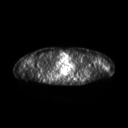
FDG PET of an extremity soft-tissue mass (from a PET/CT study), one axial slice. Position 199 of 267 along the scan axis. 128 × 128 image matrix, field of view 600 × 600 mm. Female patient, age 28 years. Case-level facts recorded for this patient, not image findings: histological type: malignant fibrous histiocytoma; grade: low; site of the primary tumour: left arm.
Outlined on this slice (expert contour drawn on MRI and transferred to this co-registered scan by the dataset authors):
- gross tumour volume (mass): bounding box (x1, y1, x2, y2) in pixels: (102, 64, 106, 69)